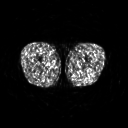
FDG PET of an extremity soft-tissue mass (from a PET/CT study), one axial slice. Slice 216 of 267 in the series (ordered by position). 3.27 mm slice thickness. 128 × 128 image matrix. Male patient, age 27 years. From the clinical record (not read from this slice): histological type: extraskeletal osteosarcoma; grade: high; site of the primary tumour: left adductur.
Outlined on this slice (expert contour drawn on MRI and transferred to this co-registered scan by the dataset authors):
- gross tumour volume (mass): bounding box (x1, y1, x2, y2) in pixels: (71, 63, 88, 70)